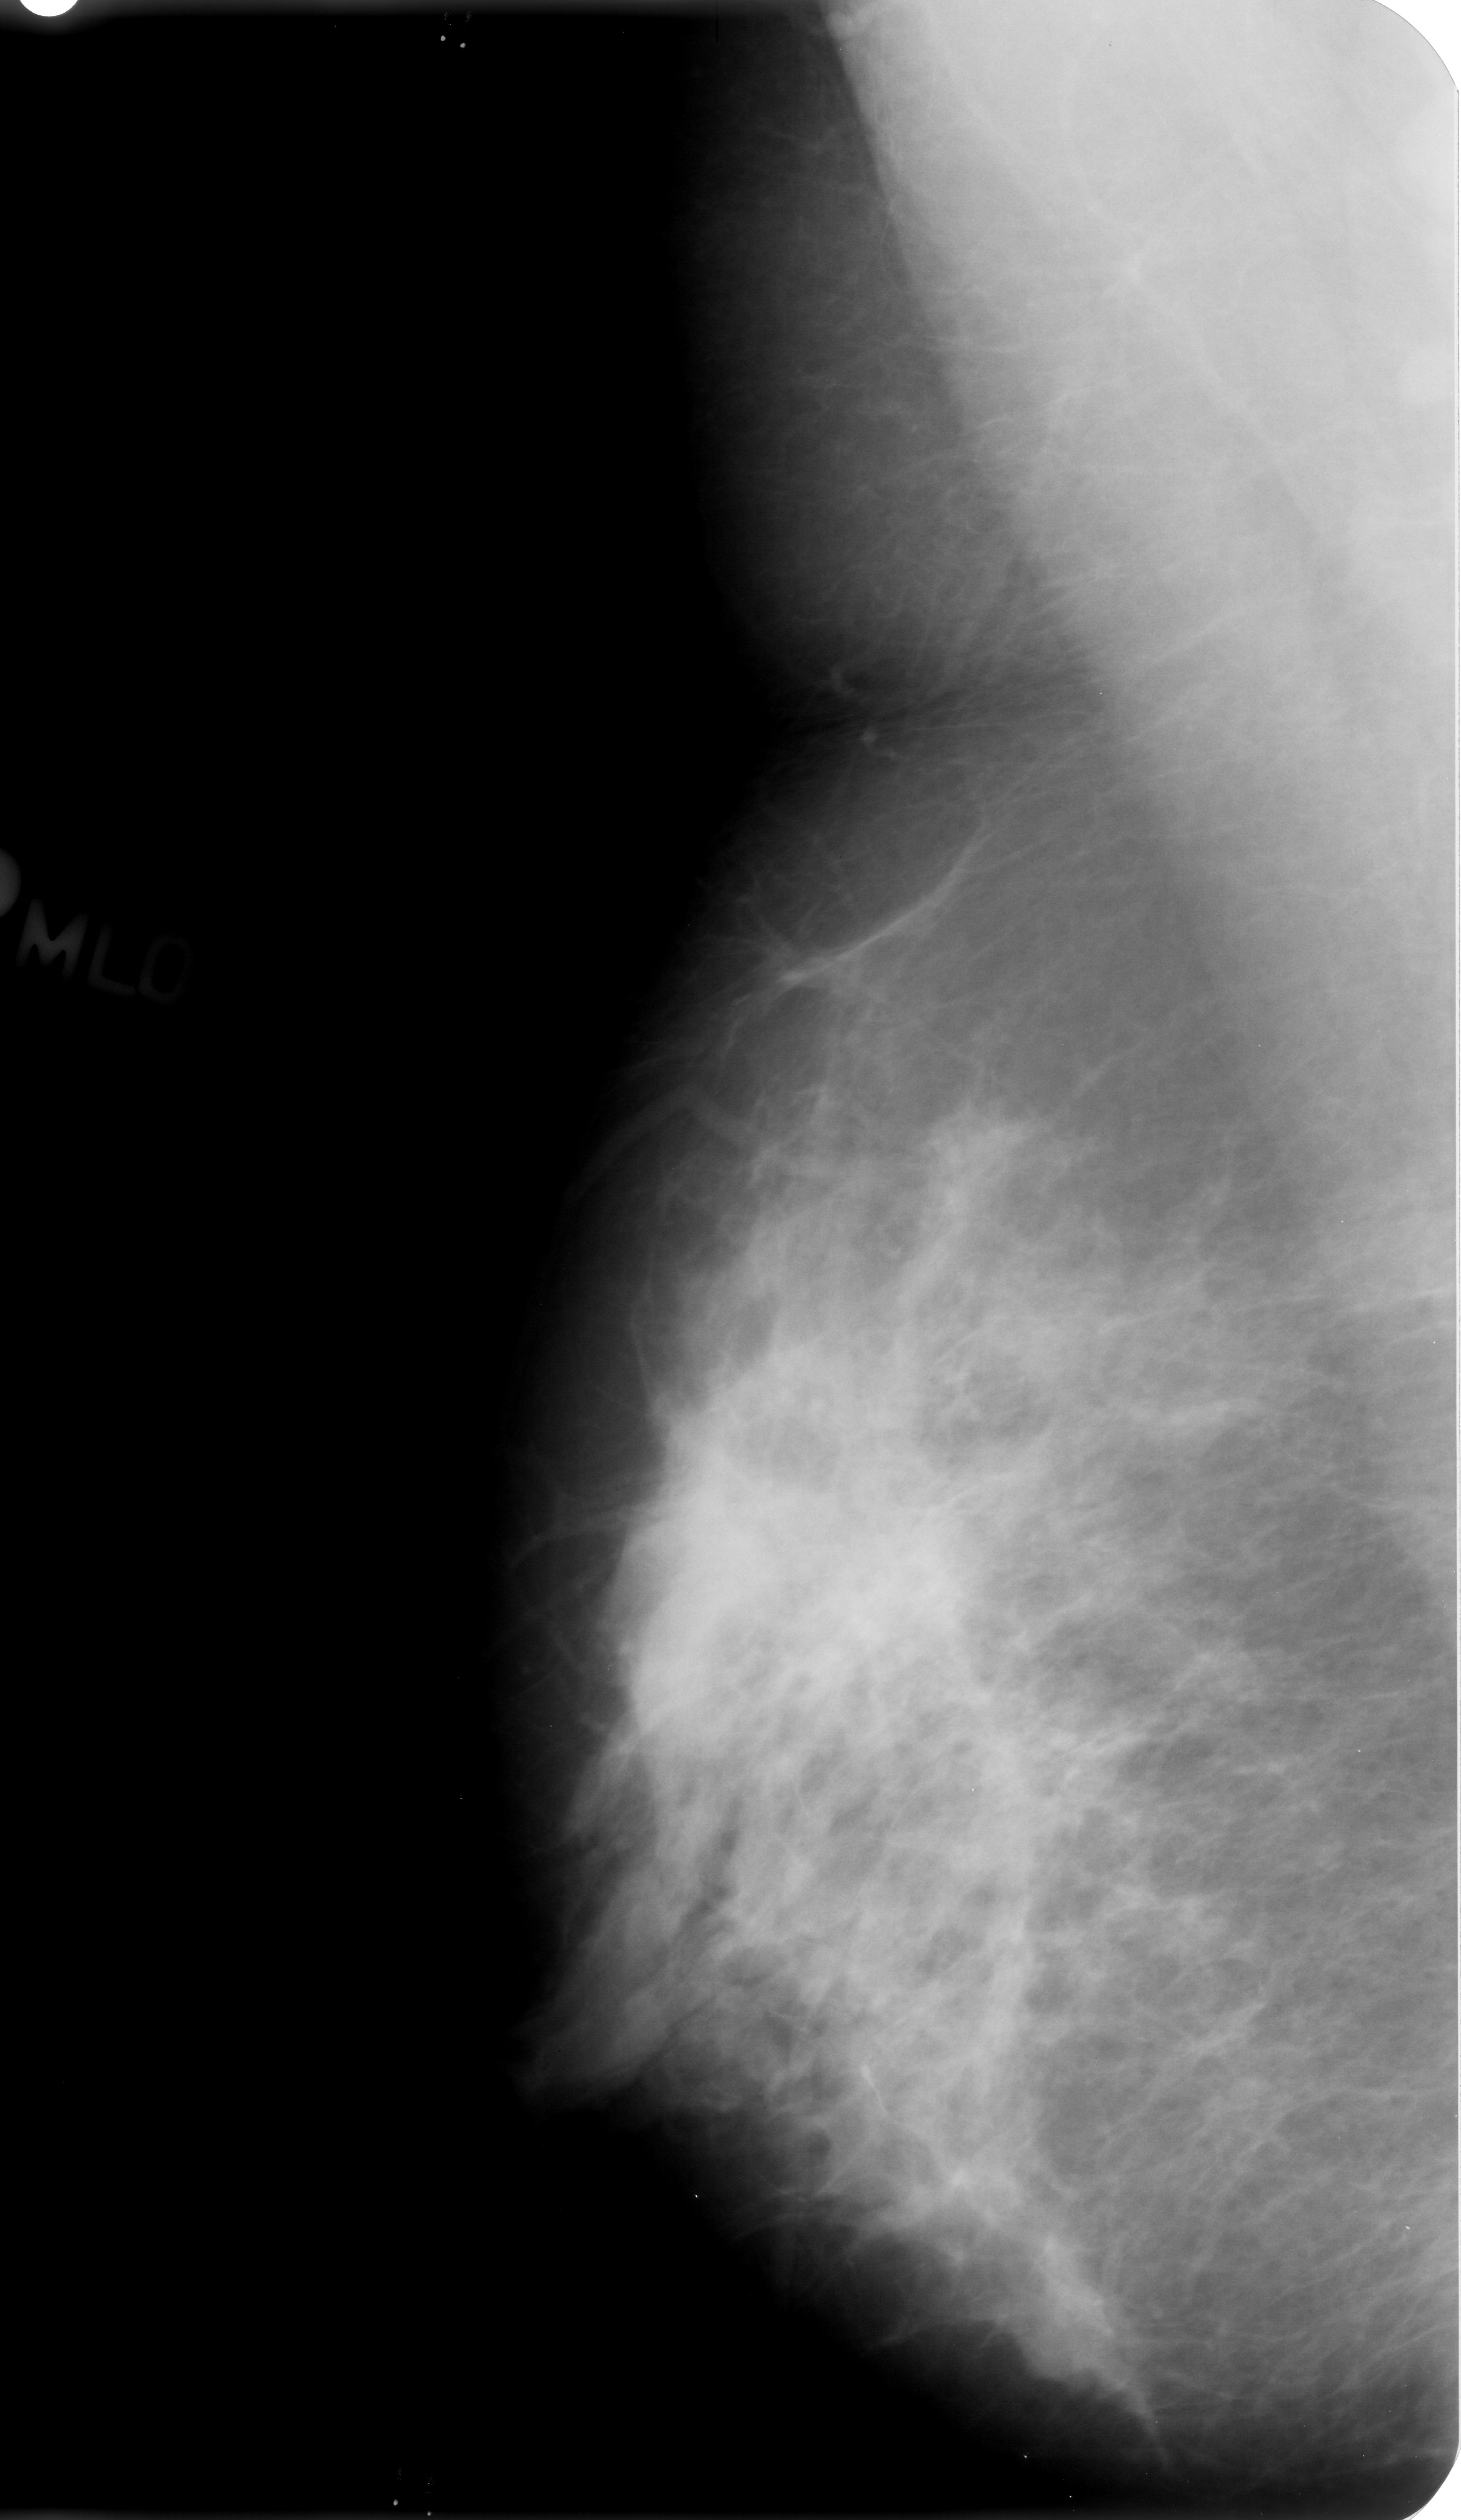
Mammogram (digitized film); right breast; mediolateral oblique (MLO) view; 1461 × 2520 image matrix.
Marked abnormalities (boxes around the expert regions of interest):
- mass, shape irregular, margins ill defined / spiculated; BI-RADS assessment category 4; pathology (as recorded): benign: bounding box (x1, y1, x2, y2) in pixels: (1008, 2246, 1144, 2397)